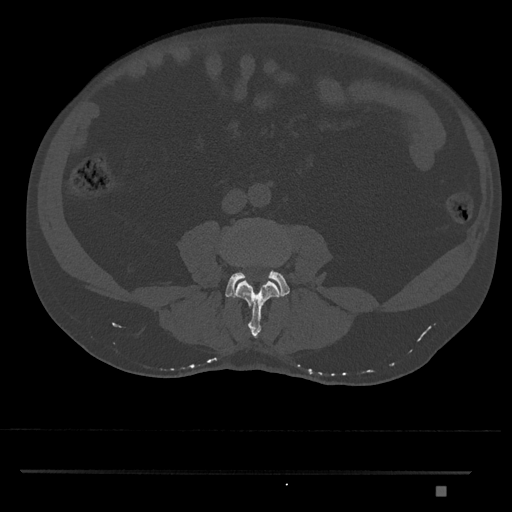
CT including the spine, one axial slice. Slice 652 of 1134 in the series (ordered by position). Reconstruction kernel Br40s/3. Bone window (W 1800 / L 400 HU). 512 × 512 image matrix, field of view 429 × 429 mm. Male patient, age 65 years. From the clinical record (not read from this slice): primary cancer: prostate.
Structures marked on this image (semi-automatic segmentation, software-assisted and operator-edited):
- L3 vertebra: box from (x=235, y=281) to (x=280, y=338) px
- L4 vertebra: (x=225, y=271)–(x=290, y=298)